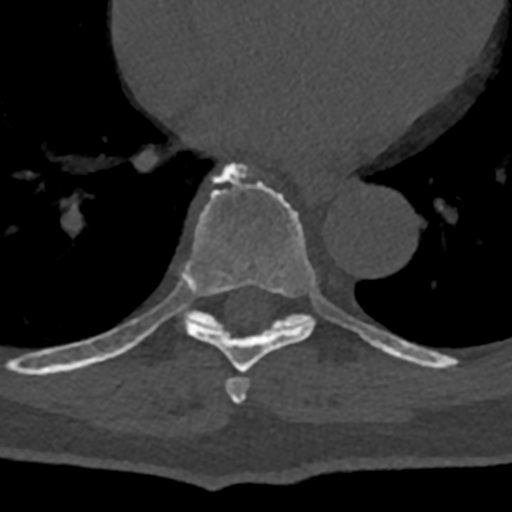
CT including the spine, one axial slice. Position 697 of 797 along the scan axis. 120 kVp. Bone window (W 1800 / L 400 HU). 0.5 mm slice thickness. 512 × 512 image matrix, field of view 160 × 160 mm. Male patient, age 74 years. From the clinical record (not read from this slice): primary cancer: renal.
Annotated regions visible in this slice (semi-automatic segmentation, software-assisted and operator-edited):
- T7 vertebra: bounding box (x1, y1, x2, y2) in pixels: (226, 377, 250, 404)
- T8 vertebra: (70, 163, 400, 373)
- T9 vertebra: (171, 282, 432, 367)